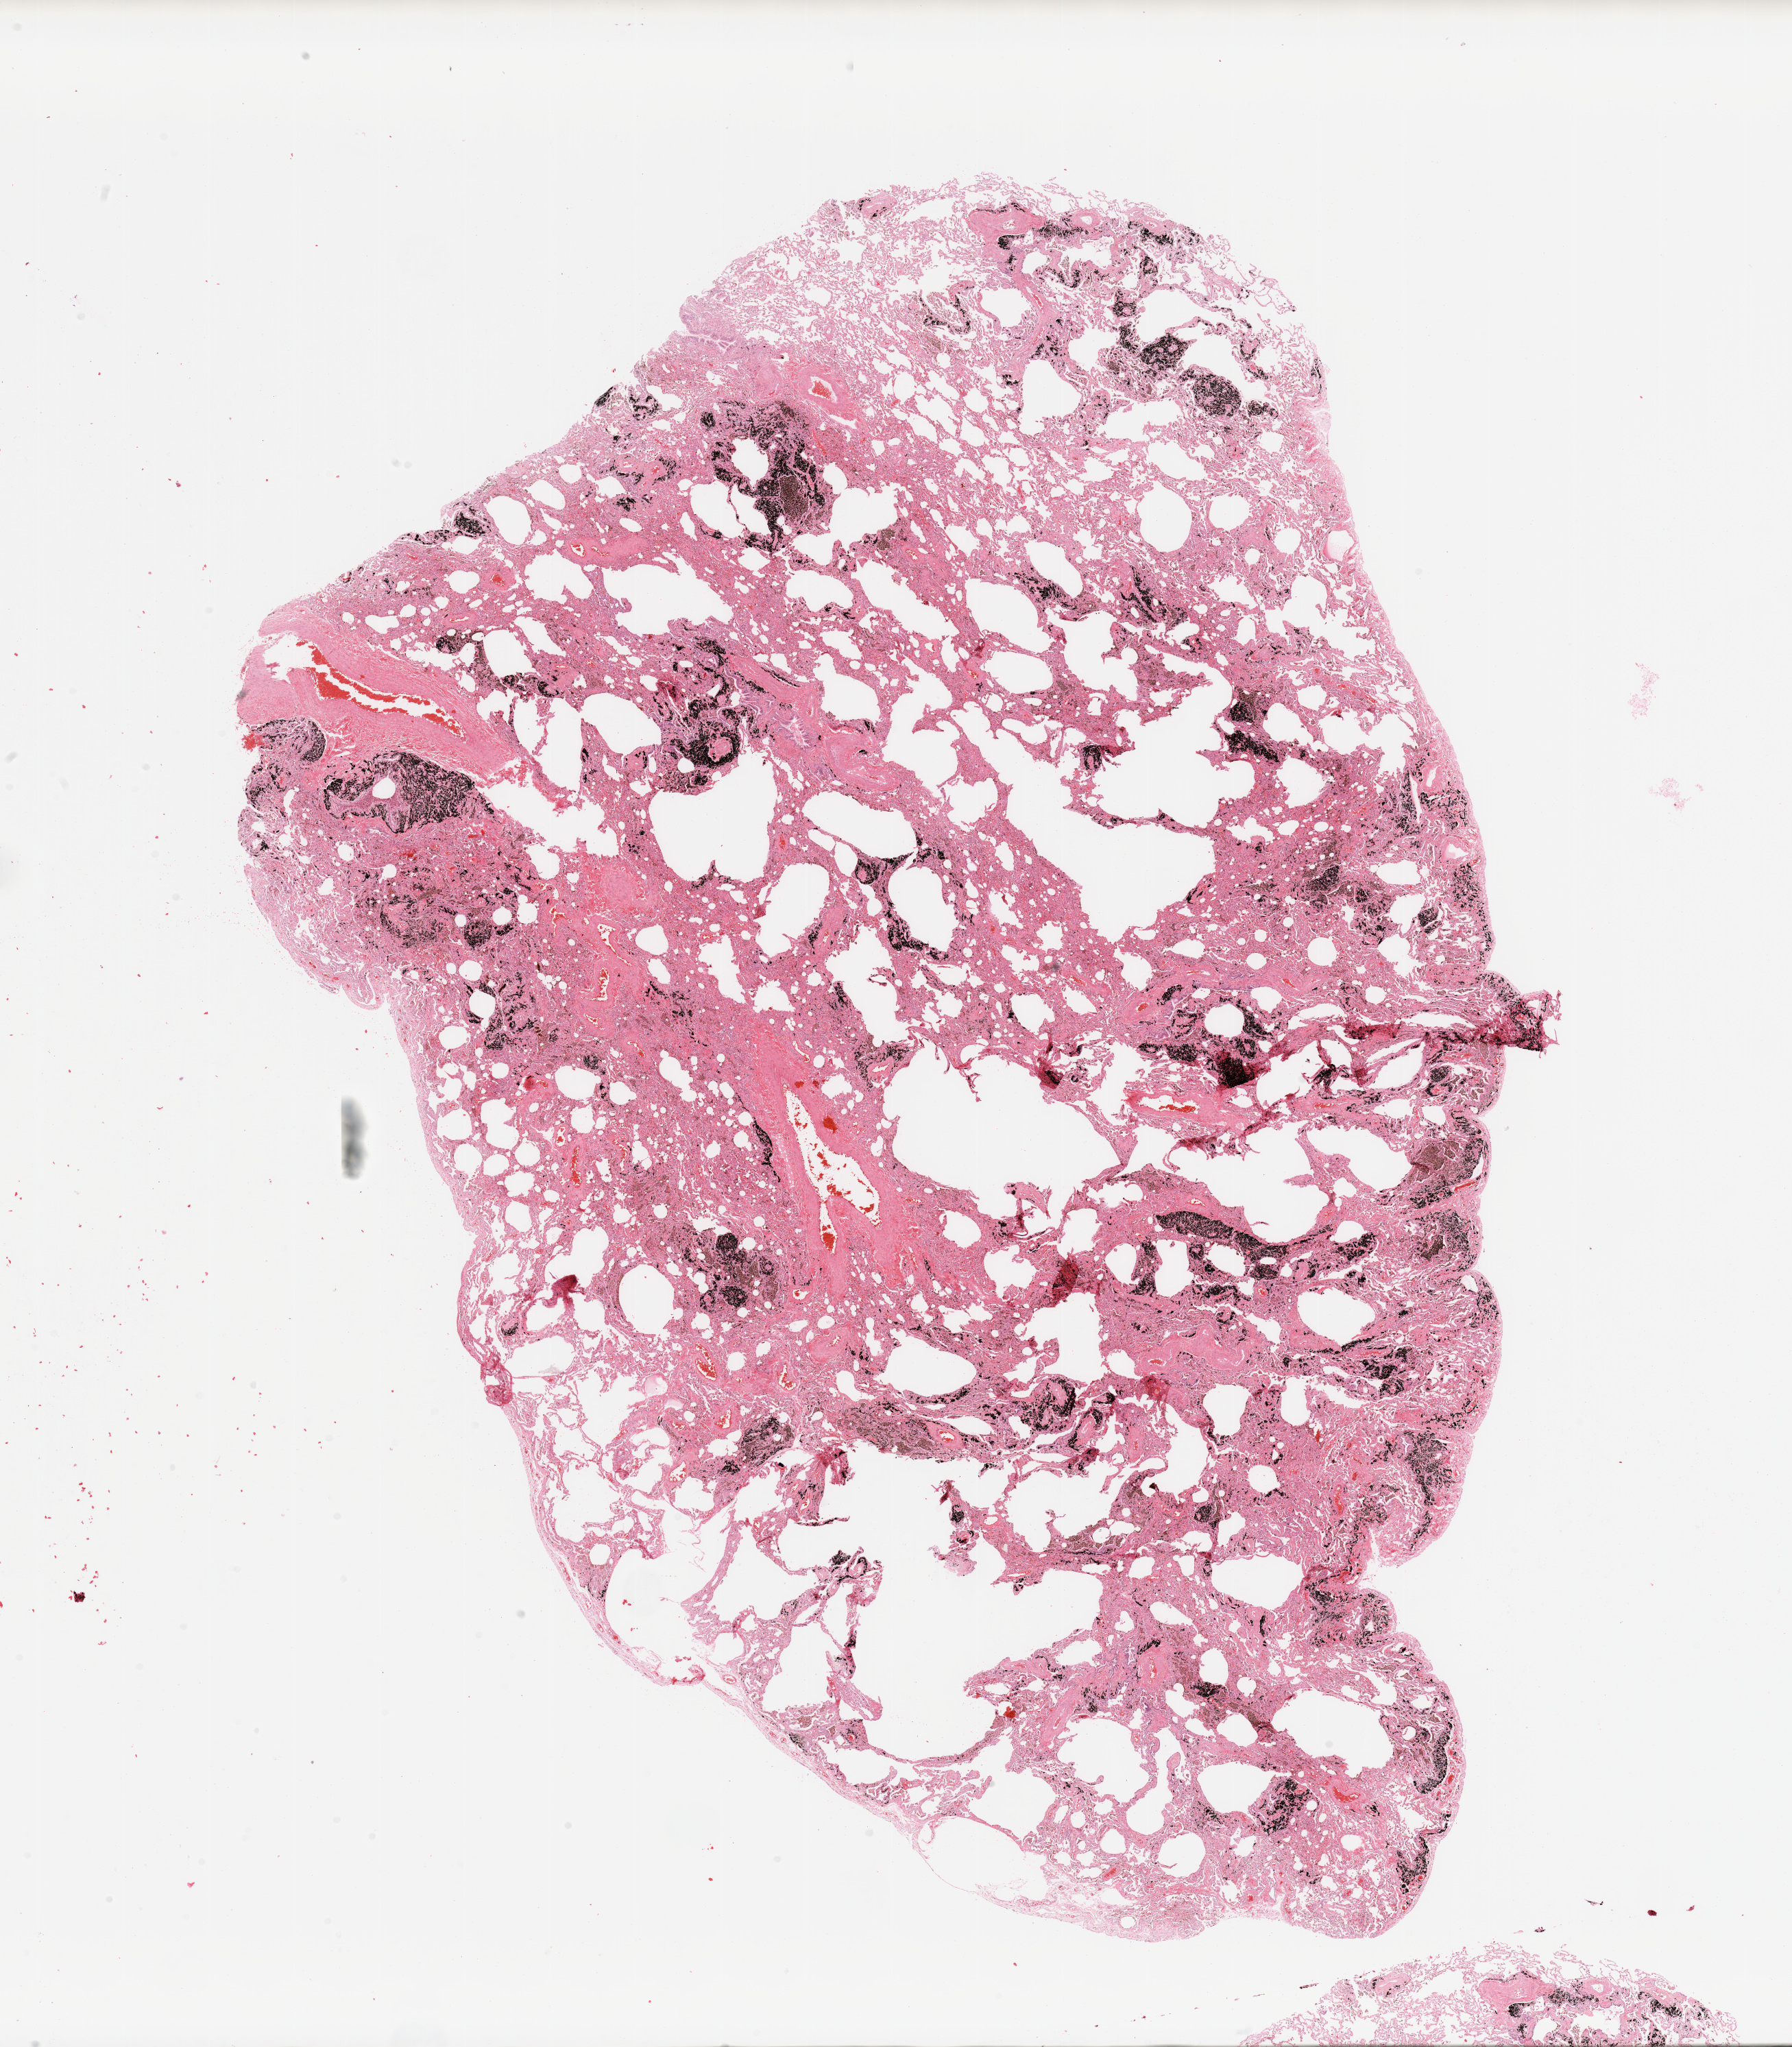
Digitized H&E-stained tissue section (whole slide) — shown as a low-resolution overview of the whole scanned area (about 20.7 x 23.6 mm, acquisition: 20x scan), lung, normal (non-tumour) tissue. Male, 56 y/o.
This section: normal (non-tumour) tissue from the same patient. Patient diagnosis: Adenocarcinoma, NOS.